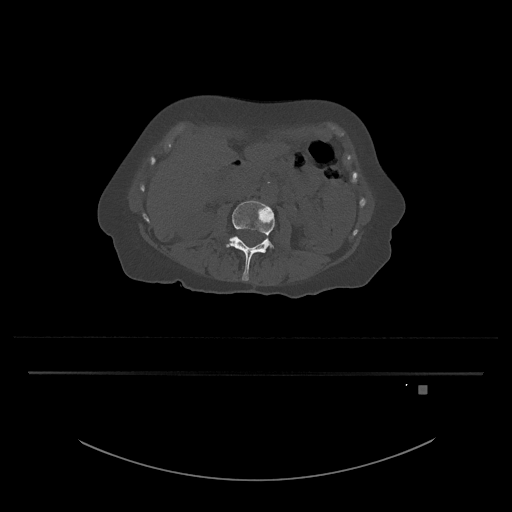
CT including the spine, one axial slice; slice 425 of 797 in the series (ordered by position); reconstruction kernel Br40s/3; 120 kVp; bone window (W 1800 / L 400 HU); 0.5 mm slice thickness; 512 × 512 image matrix, field of view 500 × 500 mm. Female patient, age 57 years. Case-level facts recorded for this patient, not image findings: primary cancer: cervical.
Annotated regions visible in this slice (semi-automatic segmentation, software-assisted and operator-edited):
- L3 vertebra: bounding box [x1, y1, x2, y2] px = [226, 200, 275, 281]